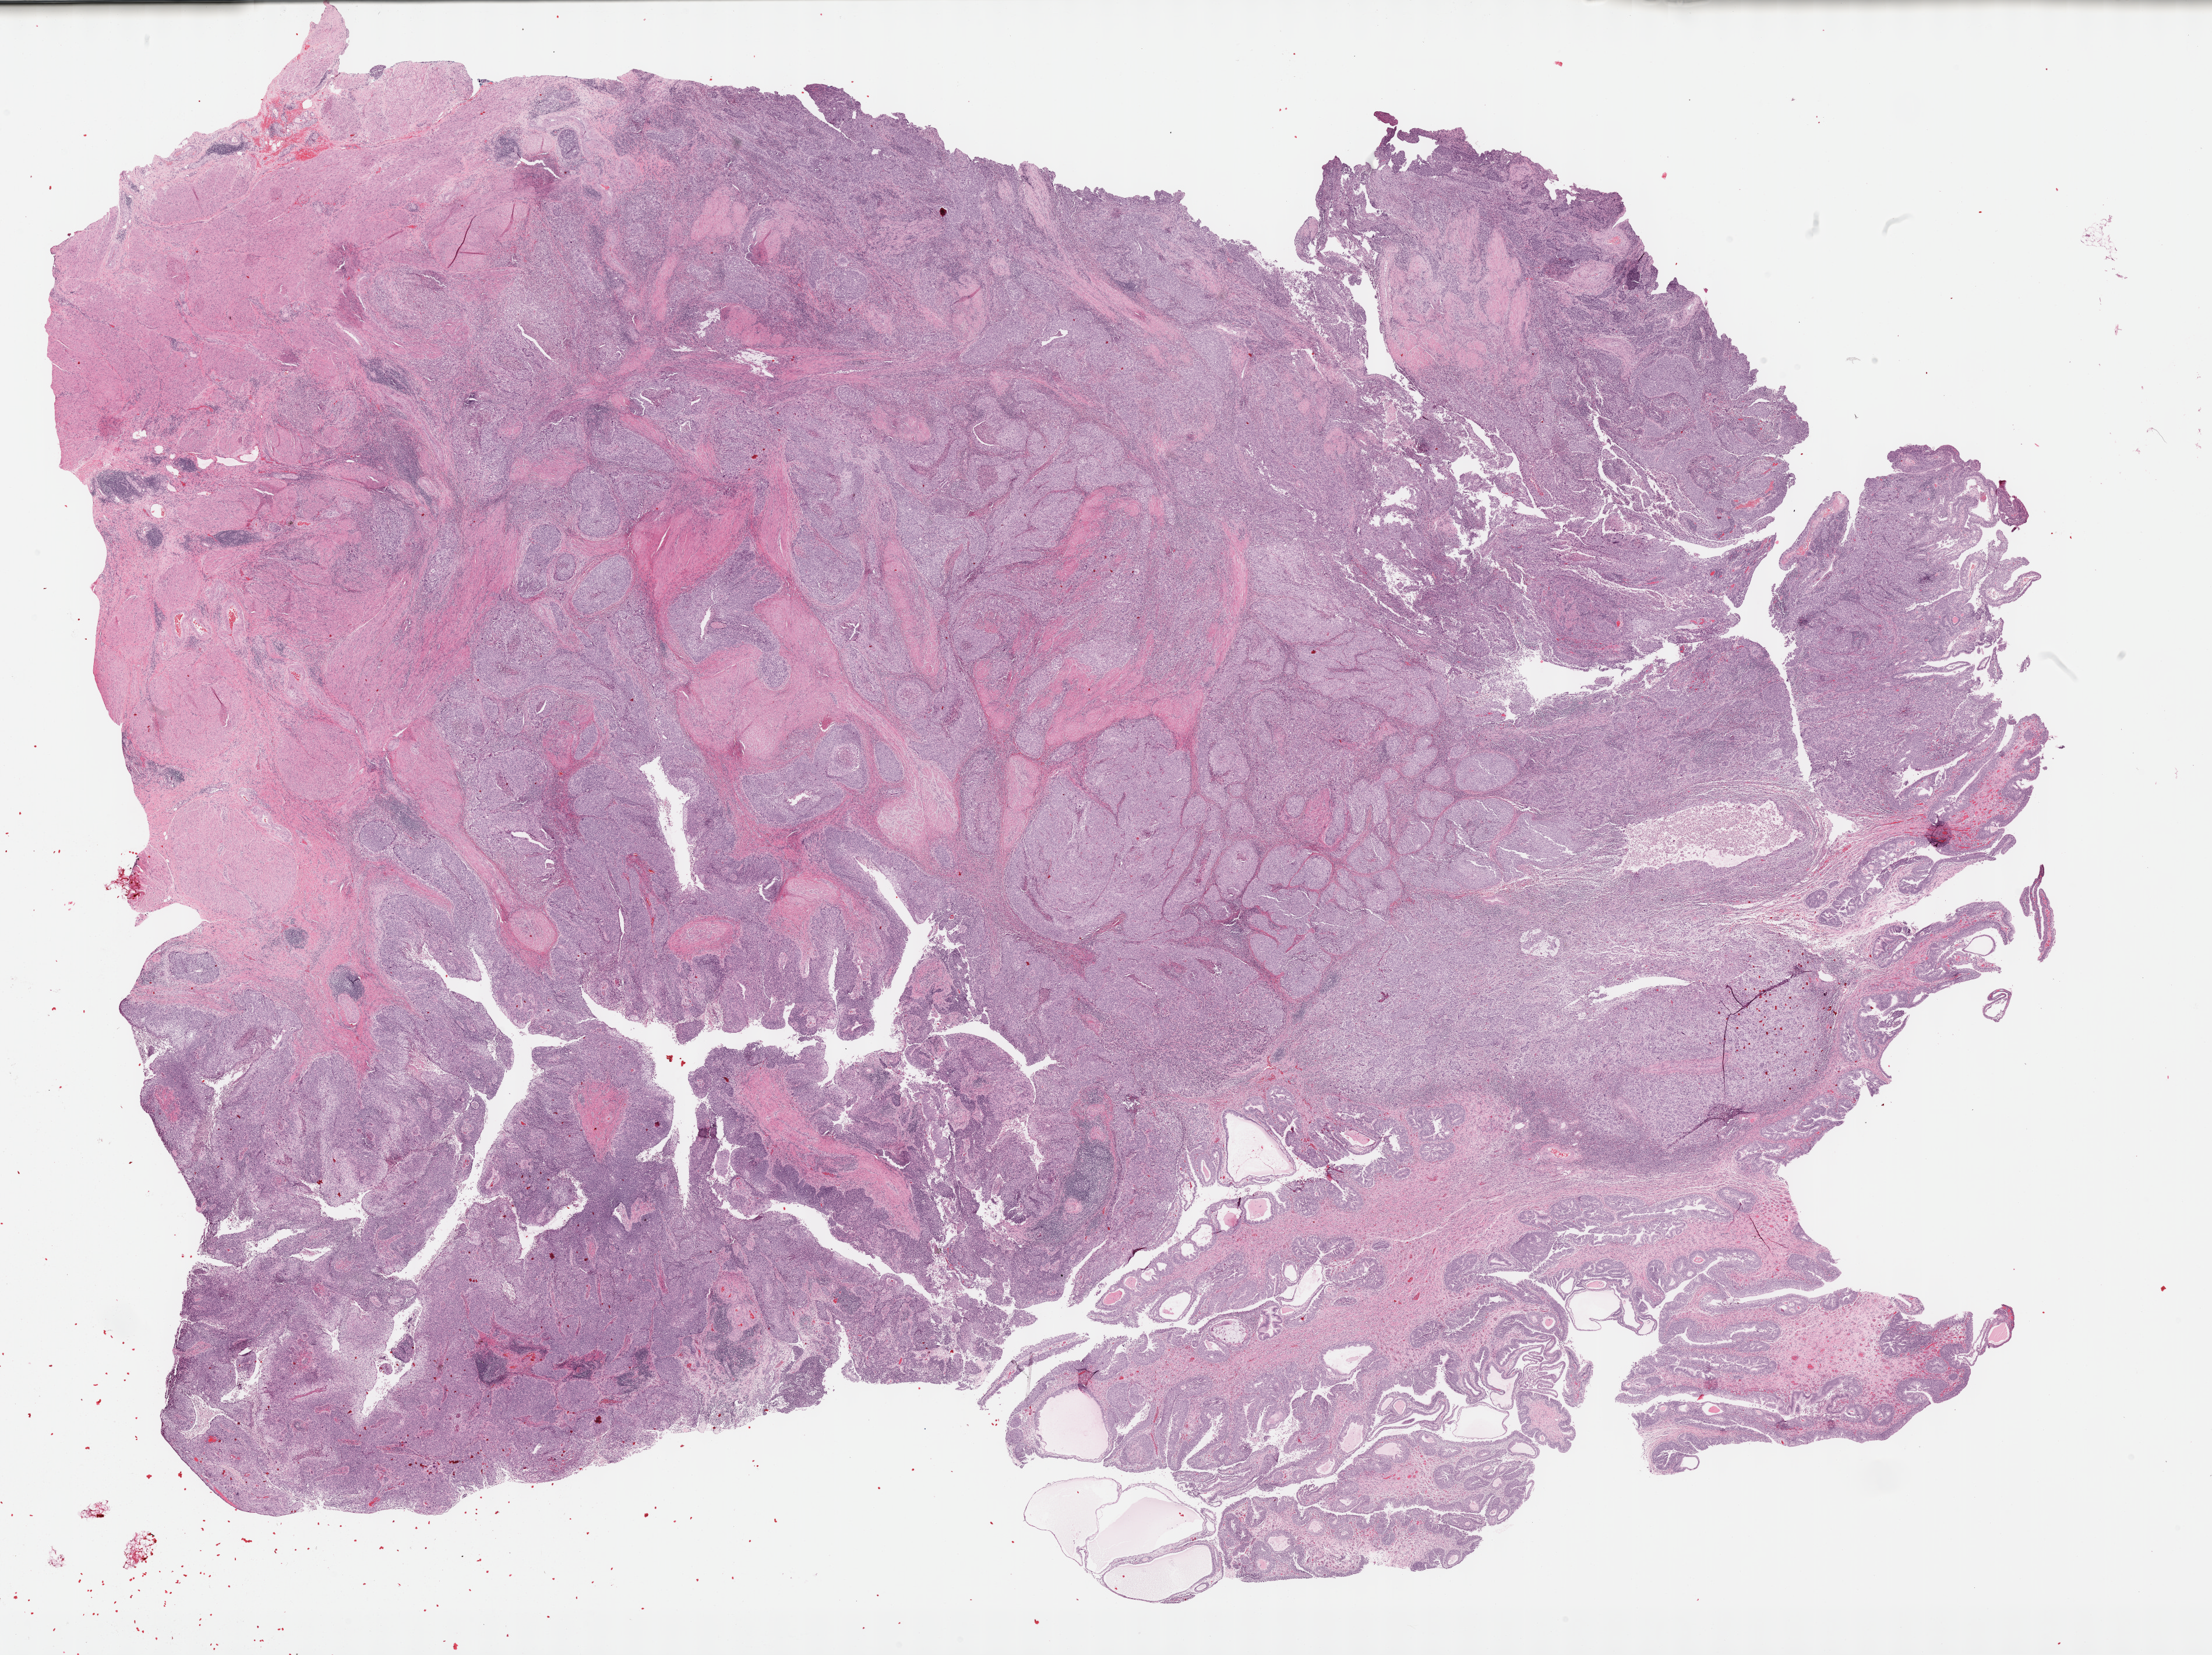
H&E whole-slide image — shown as a low-resolution overview of the whole scanned area (about 30.7 x 23.0 mm). Formalin-fixed paraffin-embedded (FFPE) diagnostic section. Bladder, primary tumour sample. Male, age 60 years at initial diagnosis. Histologic grade: high grade.
AJCC pathologic stage: II. TNM: NX M0. Pathologic diagnosis: Transitional cell carcinoma.